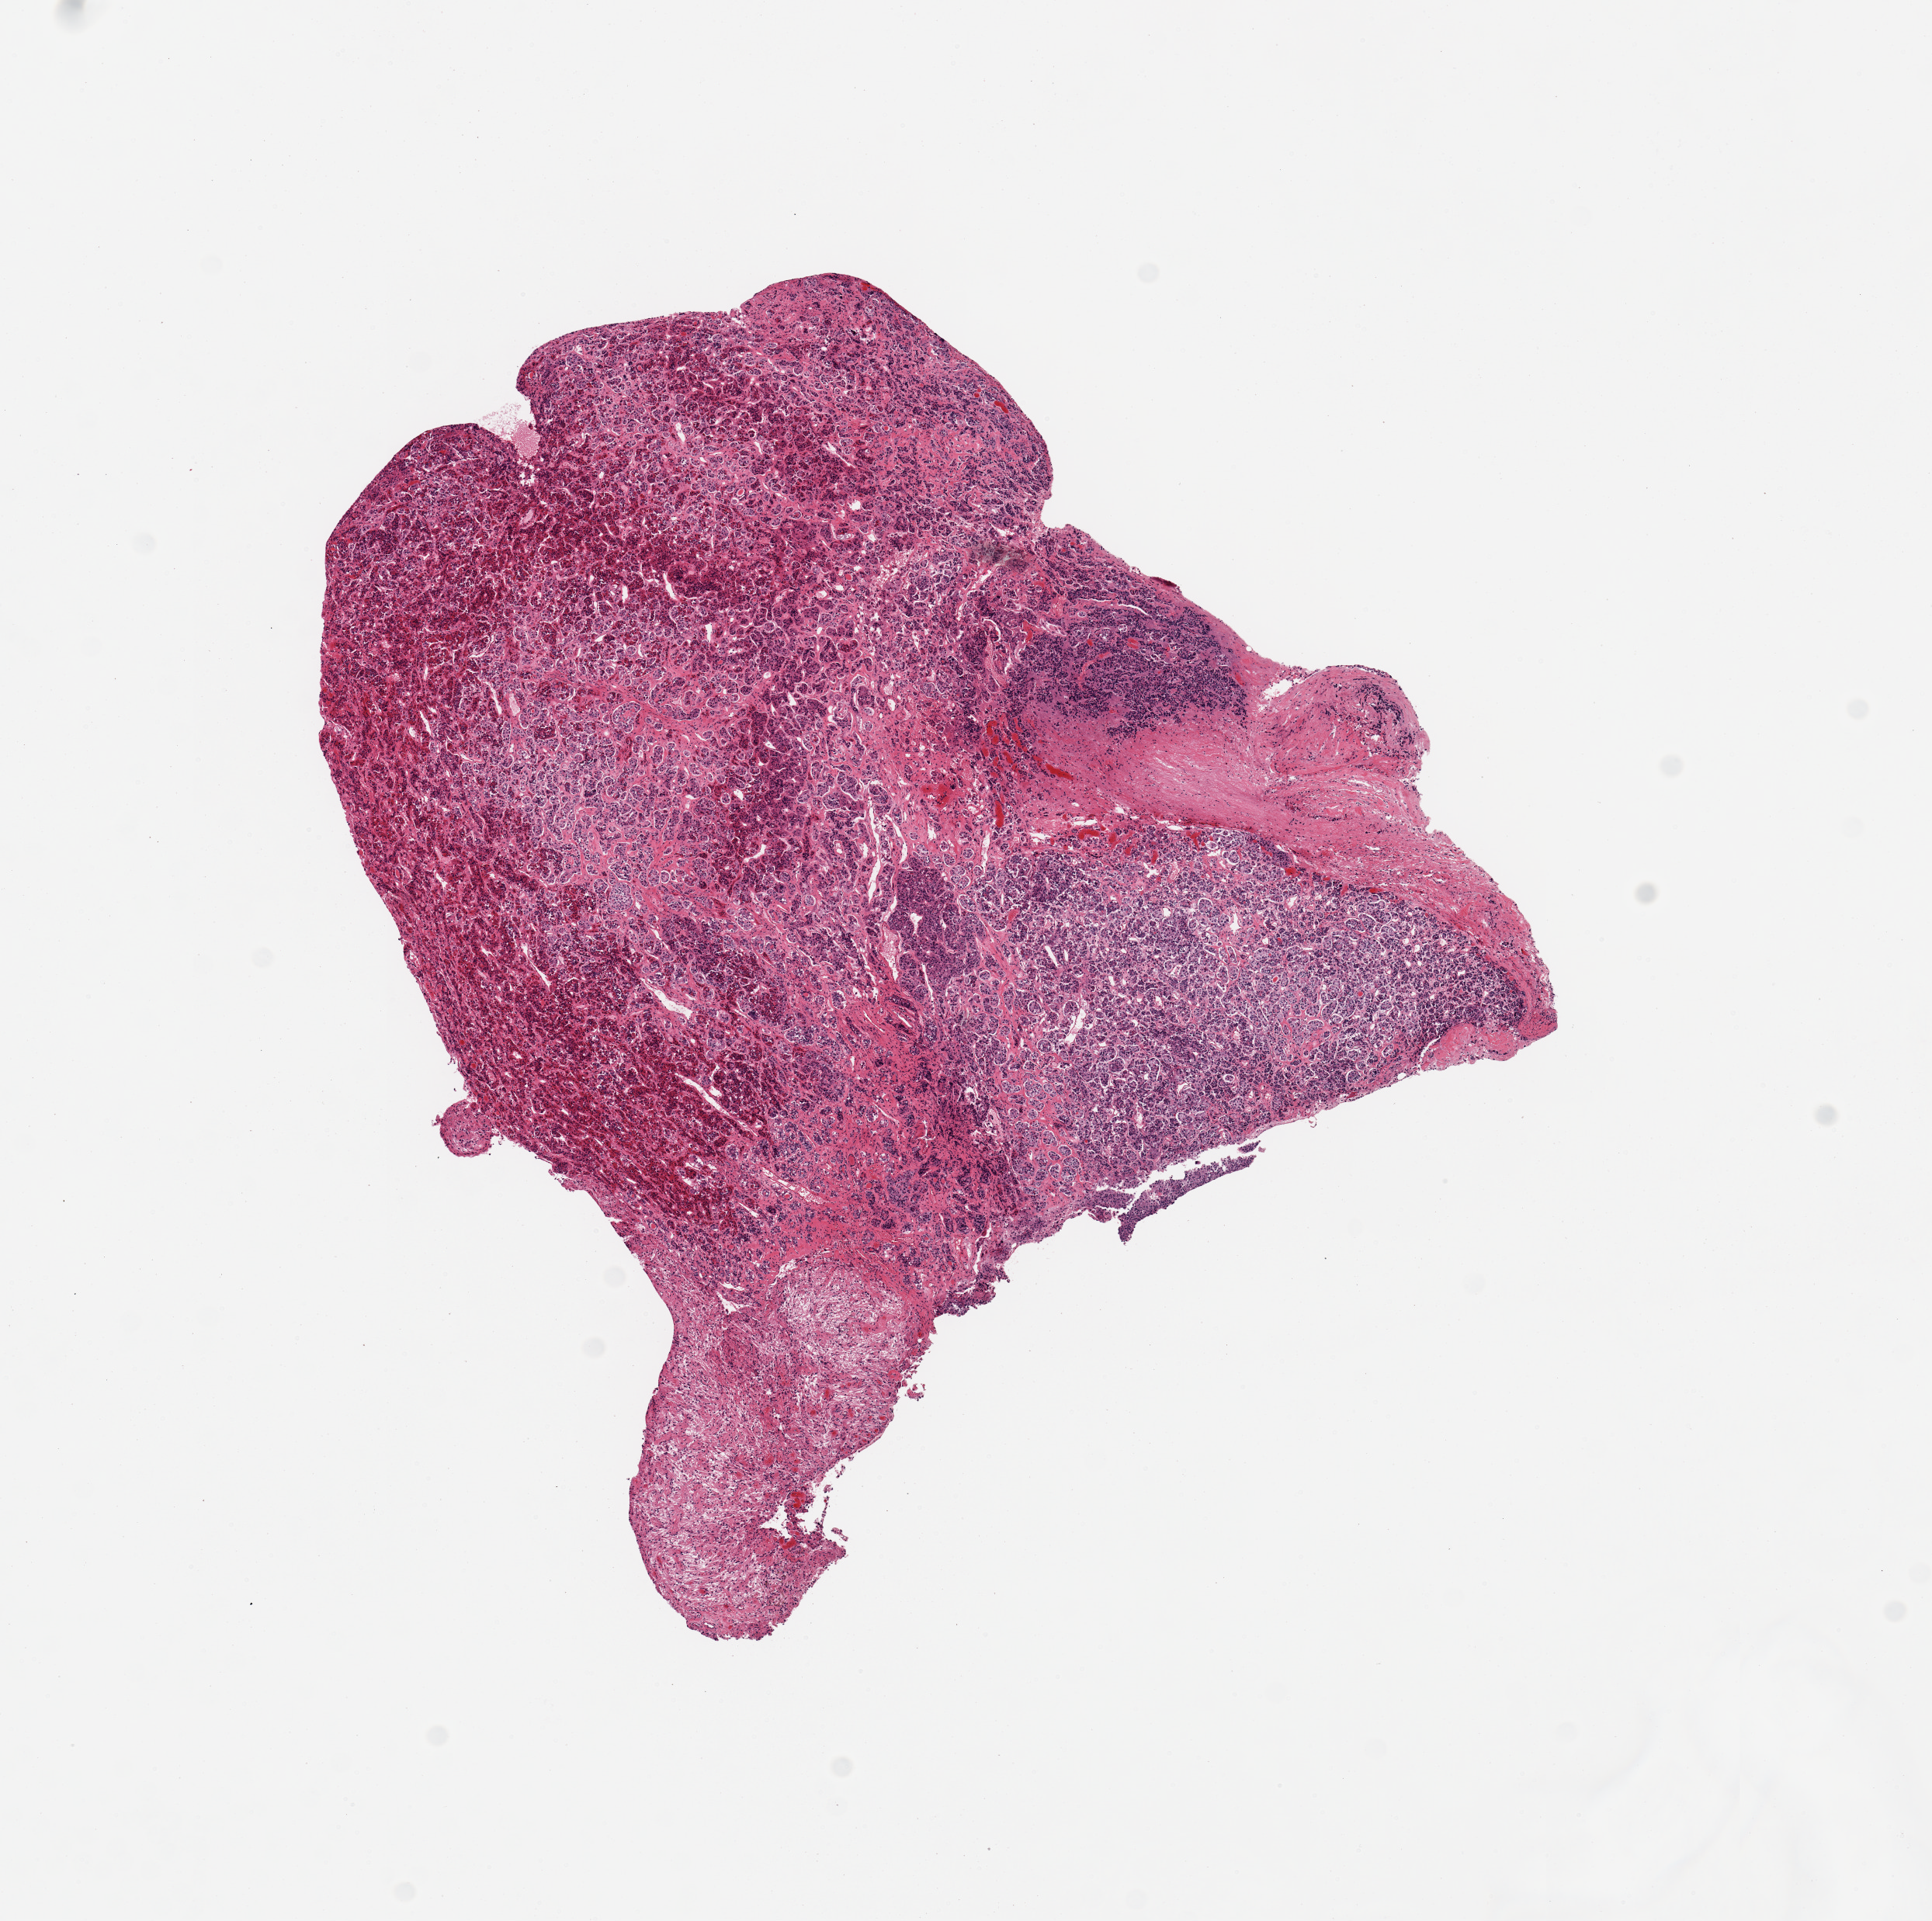
Digitized haematoxylin and eosin-stained section, a low-resolution overview of the entire scanned area, about 9.8 x 9.8 mm (acquisition: 20x scan), PAXgene-fixed paraffin-embedded (PFPE) section, section of pituitary (target tissue), donor tissue sample. Male donor.
* reviewer comment on this tissue sample: 1 piece, ~2x1mm nubbin of neurohypophysis, rest is adenohypophysis